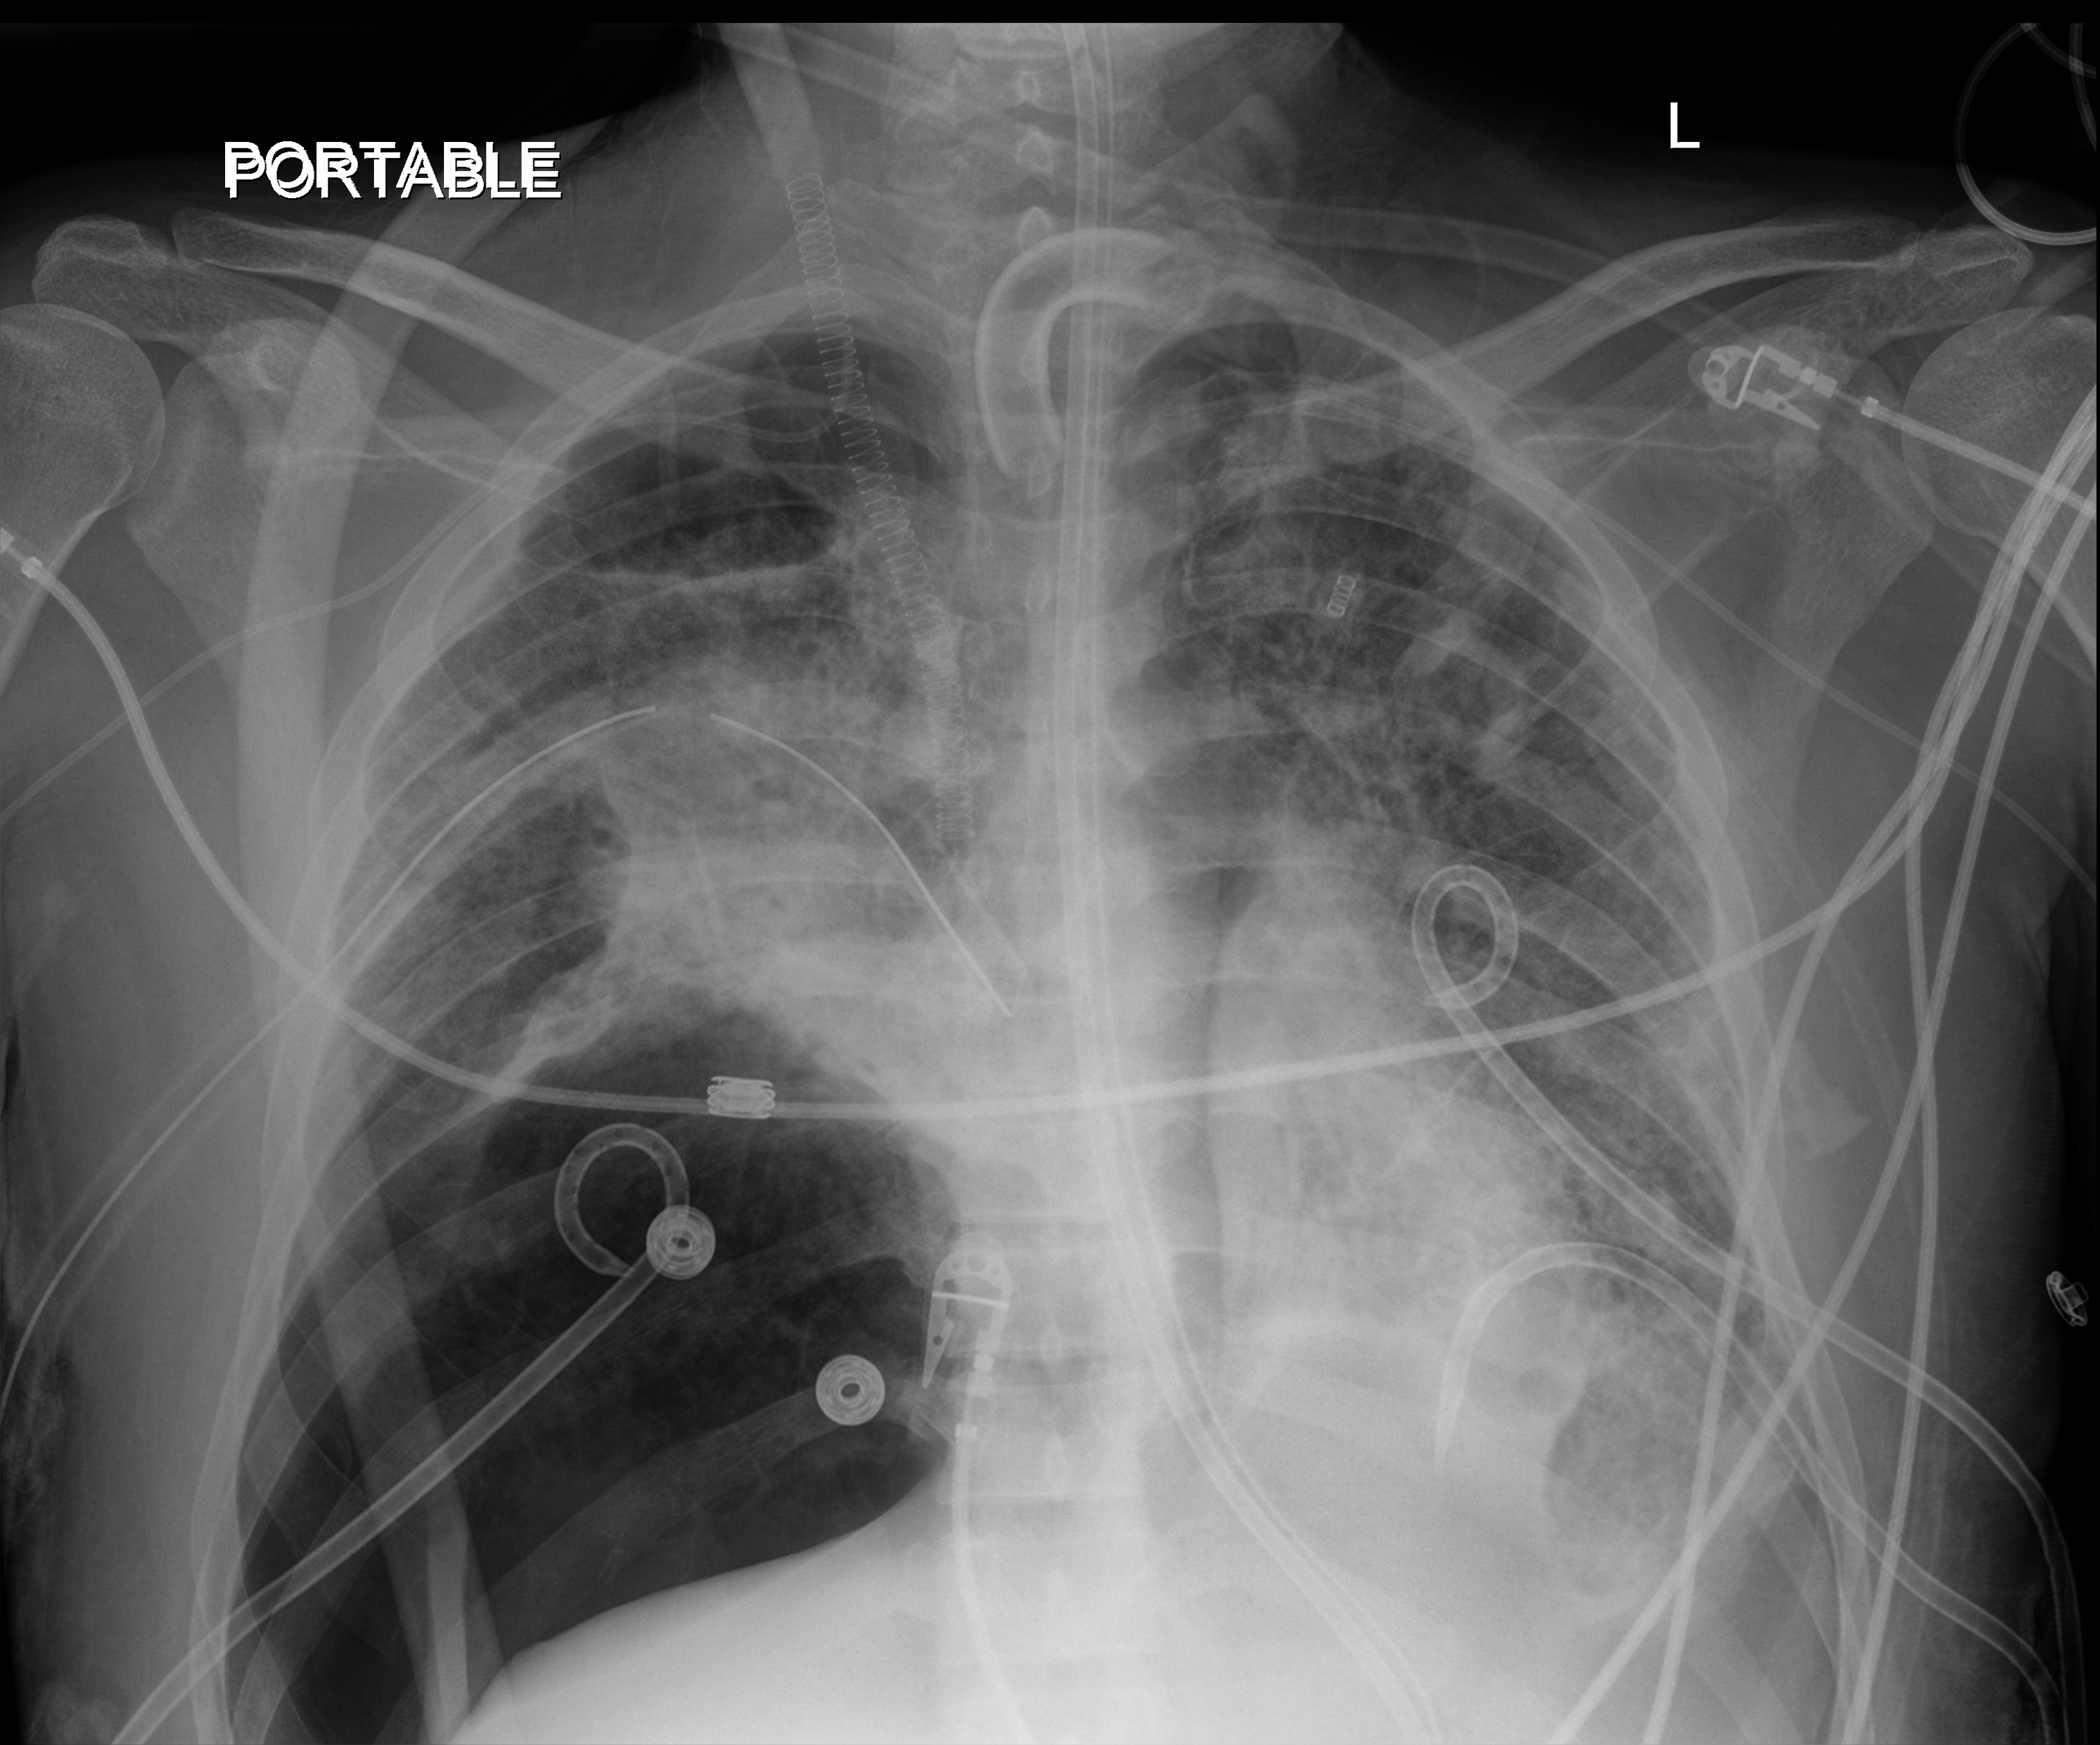
Chest X-ray (portable). Patient hospitalised with COVID-19, aged 18–59 years.
Hospital-stay facts (about this admission, not read from this image; timing relative to this image not recorded):
- admitted to intensive care during this hospital stay: yes
- other chronic lung disease (admission record): no